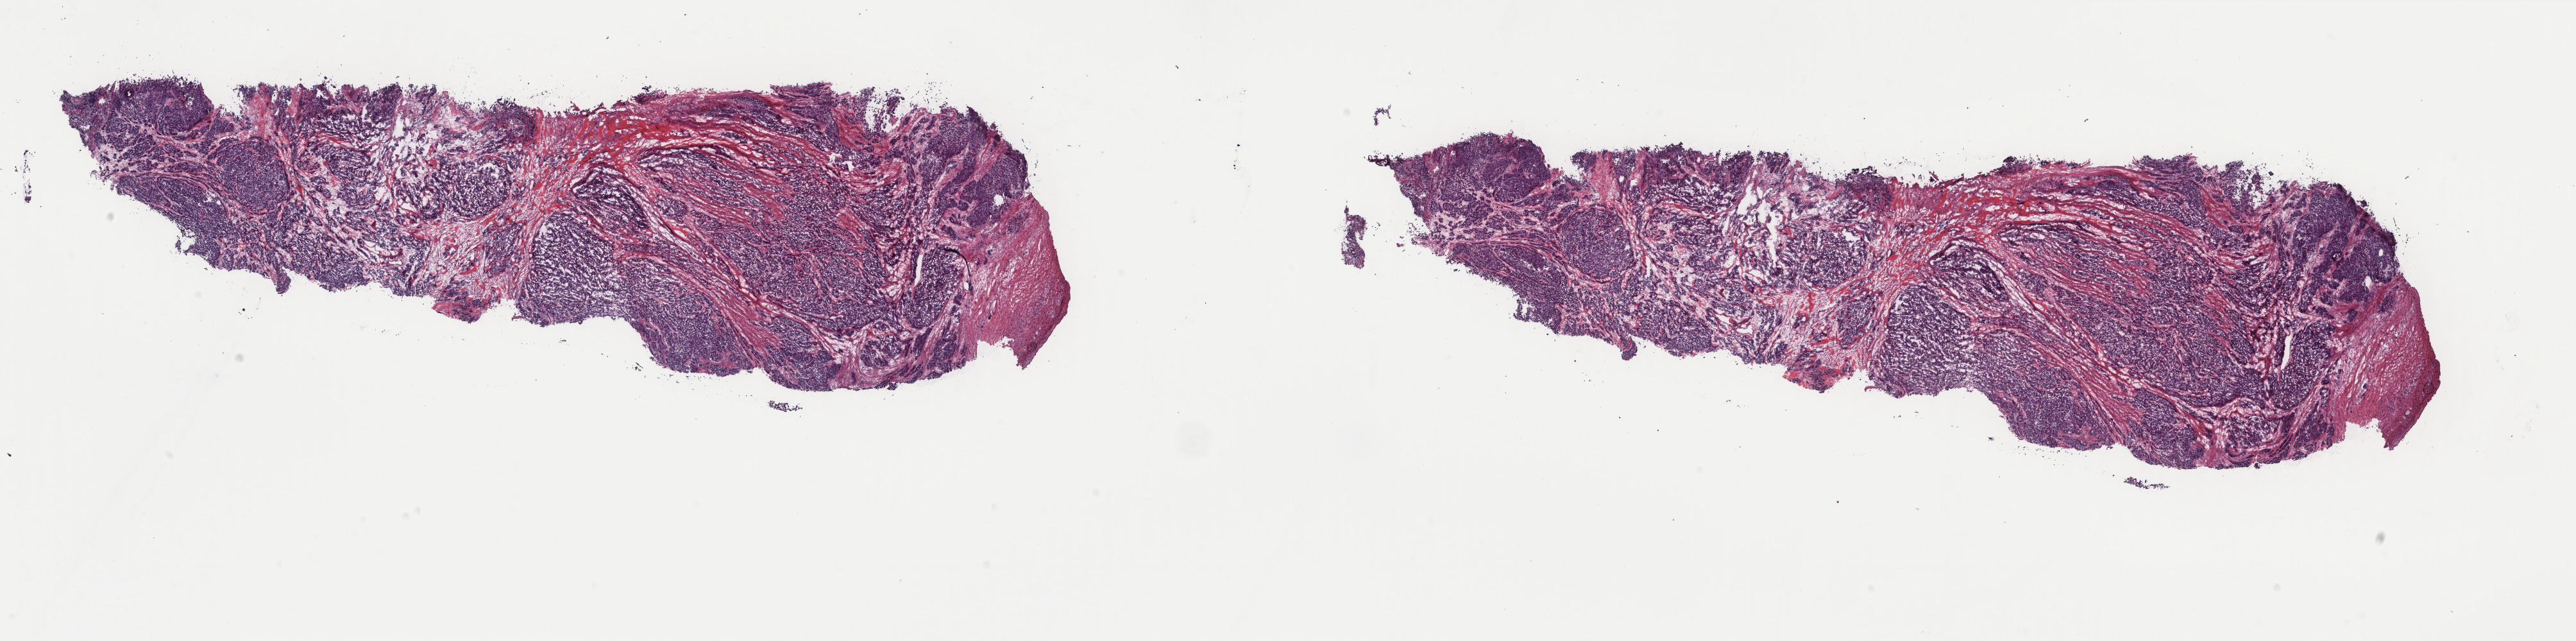
Digitized H&E tissue section (whole slide), whole scanned area (about 31.9 x 7.9 mm, from a 40x scan) shown as a low-resolution overview. Frozen section from the top of the tissue portion. Primary tumour sample from the stomach. Female patient; age at initial diagnosis 70 years. Histologic grade: G3 (poorly differentiated). Slide review estimates, as recorded: tumour cells 65%, tumour nuclei 85%, normal cells 0%, stromal cells 33%, necrosis 2%. Inflammatory infiltration, as recorded: lymphocyte infiltration 4%, monocyte infiltration 0%, neutrophil infiltration 0%.
Pathologic diagnosis: Adenocarcinoma, NOS (fundus of stomach). Lymph nodes positive (case pathology): 8 of 8 examined. AJCC pathologic stage: IIIC.